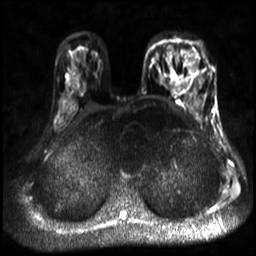
Breast MRI, one axial slice; slice 20 of 30 in the series (ordered by position); diffusion-weighted series; image 2 of 4 stored at this slice position (different b-values; order by instance number); 3 T; 256 × 256 image matrix, field of view 320 × 320 mm. Female patient.
Annotated regions visible in this slice (expert manual segmentation):
- tumour on diffusion-weighted imaging: box from (x=185, y=52) to (x=201, y=73) px